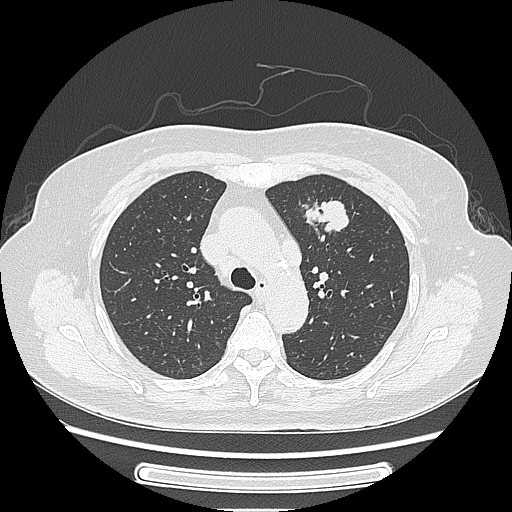
Chest CT, one axial slice; slice 170 of 227 in the series (ordered by position); lung window (W 1500 / L -600 HU); 1.25 mm slice thickness; 512 × 512 image matrix, field of view 363 × 363 mm. Patient: female, 77 years. Case-level facts recorded for this patient, not image findings: clinical TNM (as recorded): T1c N3 M0; histopathological grade: G2-3.
Structures marked on this image (rectangle marked by the reading radiologist):
- lung tumour (recorded histology: adenocarcinoma): bounding box <304,191,360,246> (left, top, right, bottom; pixels)